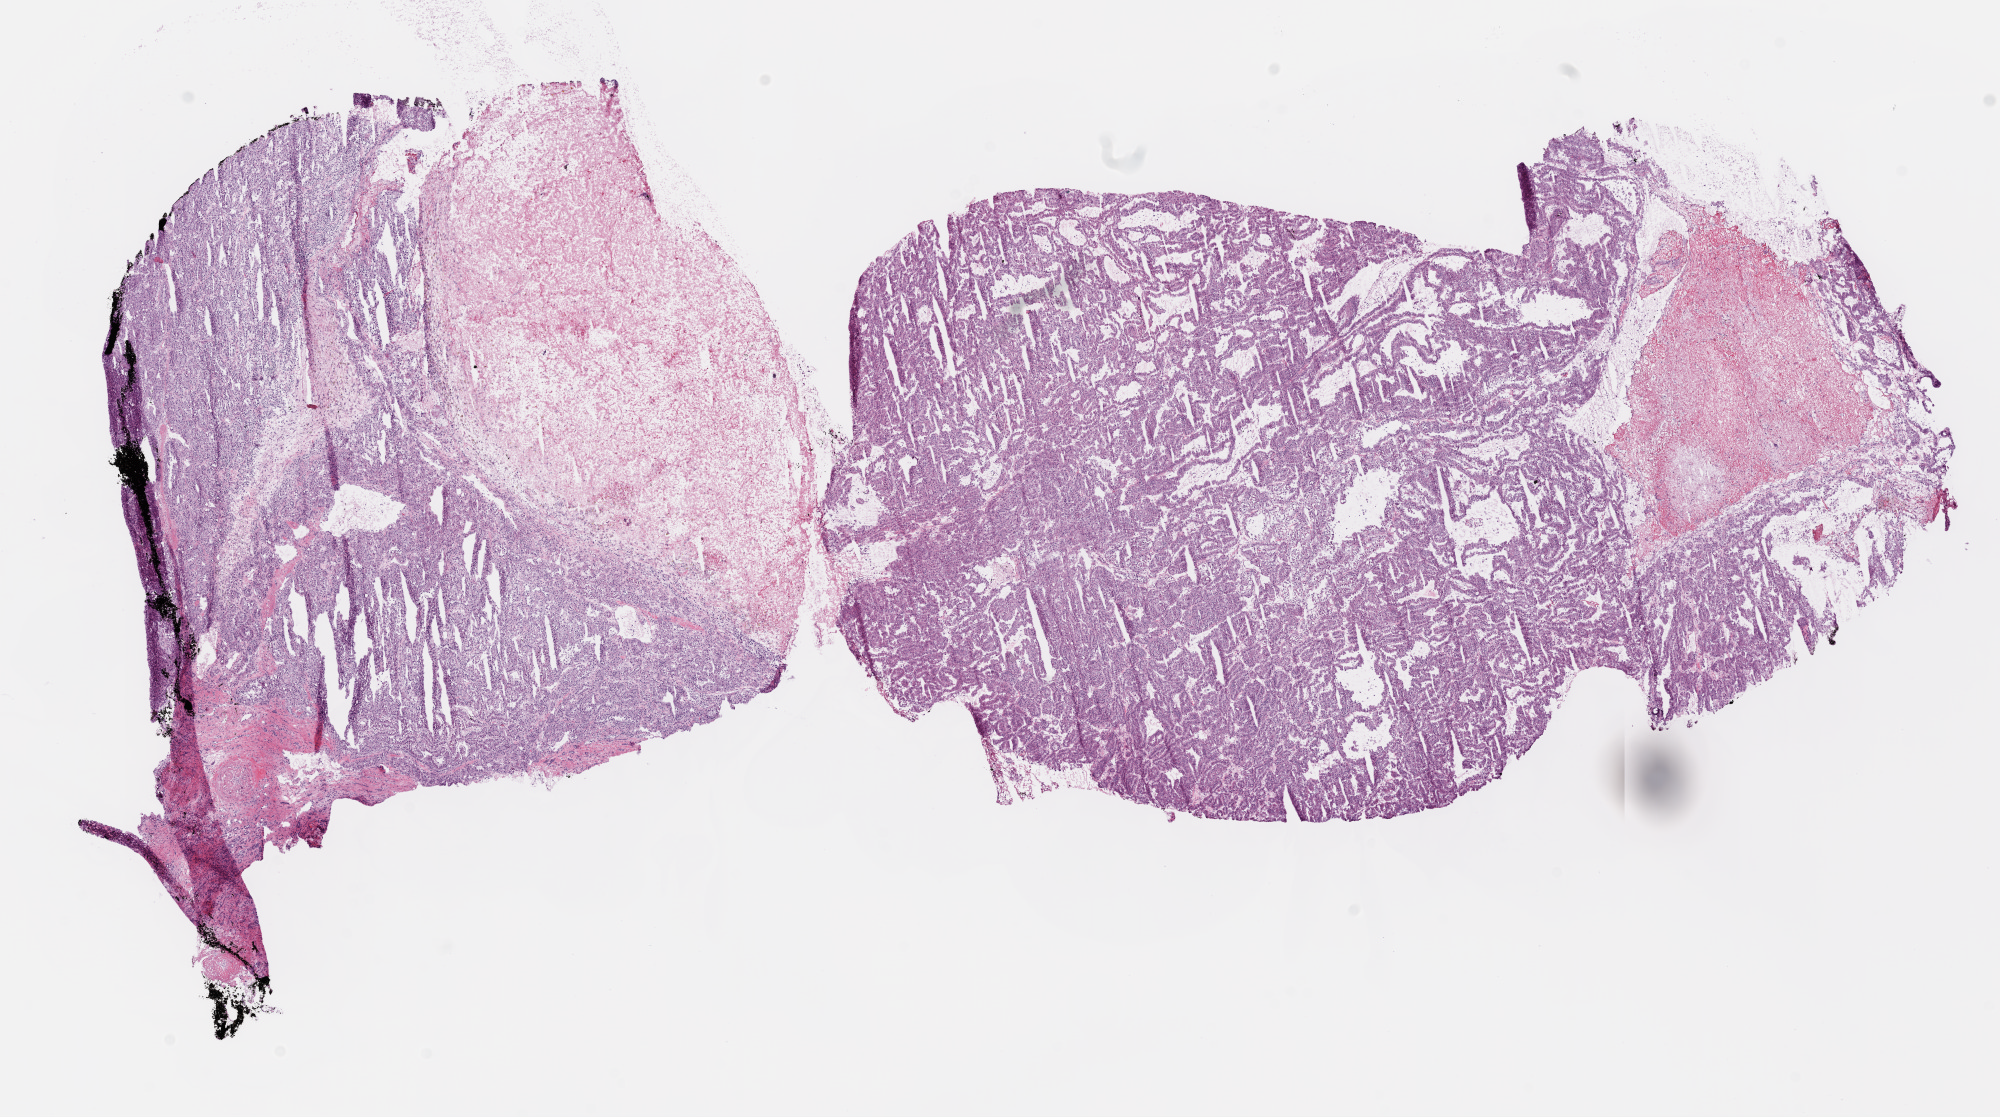
Digitized H&E tissue section (whole slide) — a low-resolution overview of the entire scanned area, about 16.0 x 9.0 mm (slide scanned at 20x), frozen section, sample: primary tumour, kidney. Male patient; age at initial diagnosis 59 years. Histologic grade: G3 (poorly differentiated). Composition of this section per pathologist review: tumour cells 70%, tumour nuclei 85%, normal cells 0%, stromal cells 5%, necrosis 25%.
Histologic diagnosis: Clear cell adenocarcinoma, NOS. AJCC pathologic stage: I.